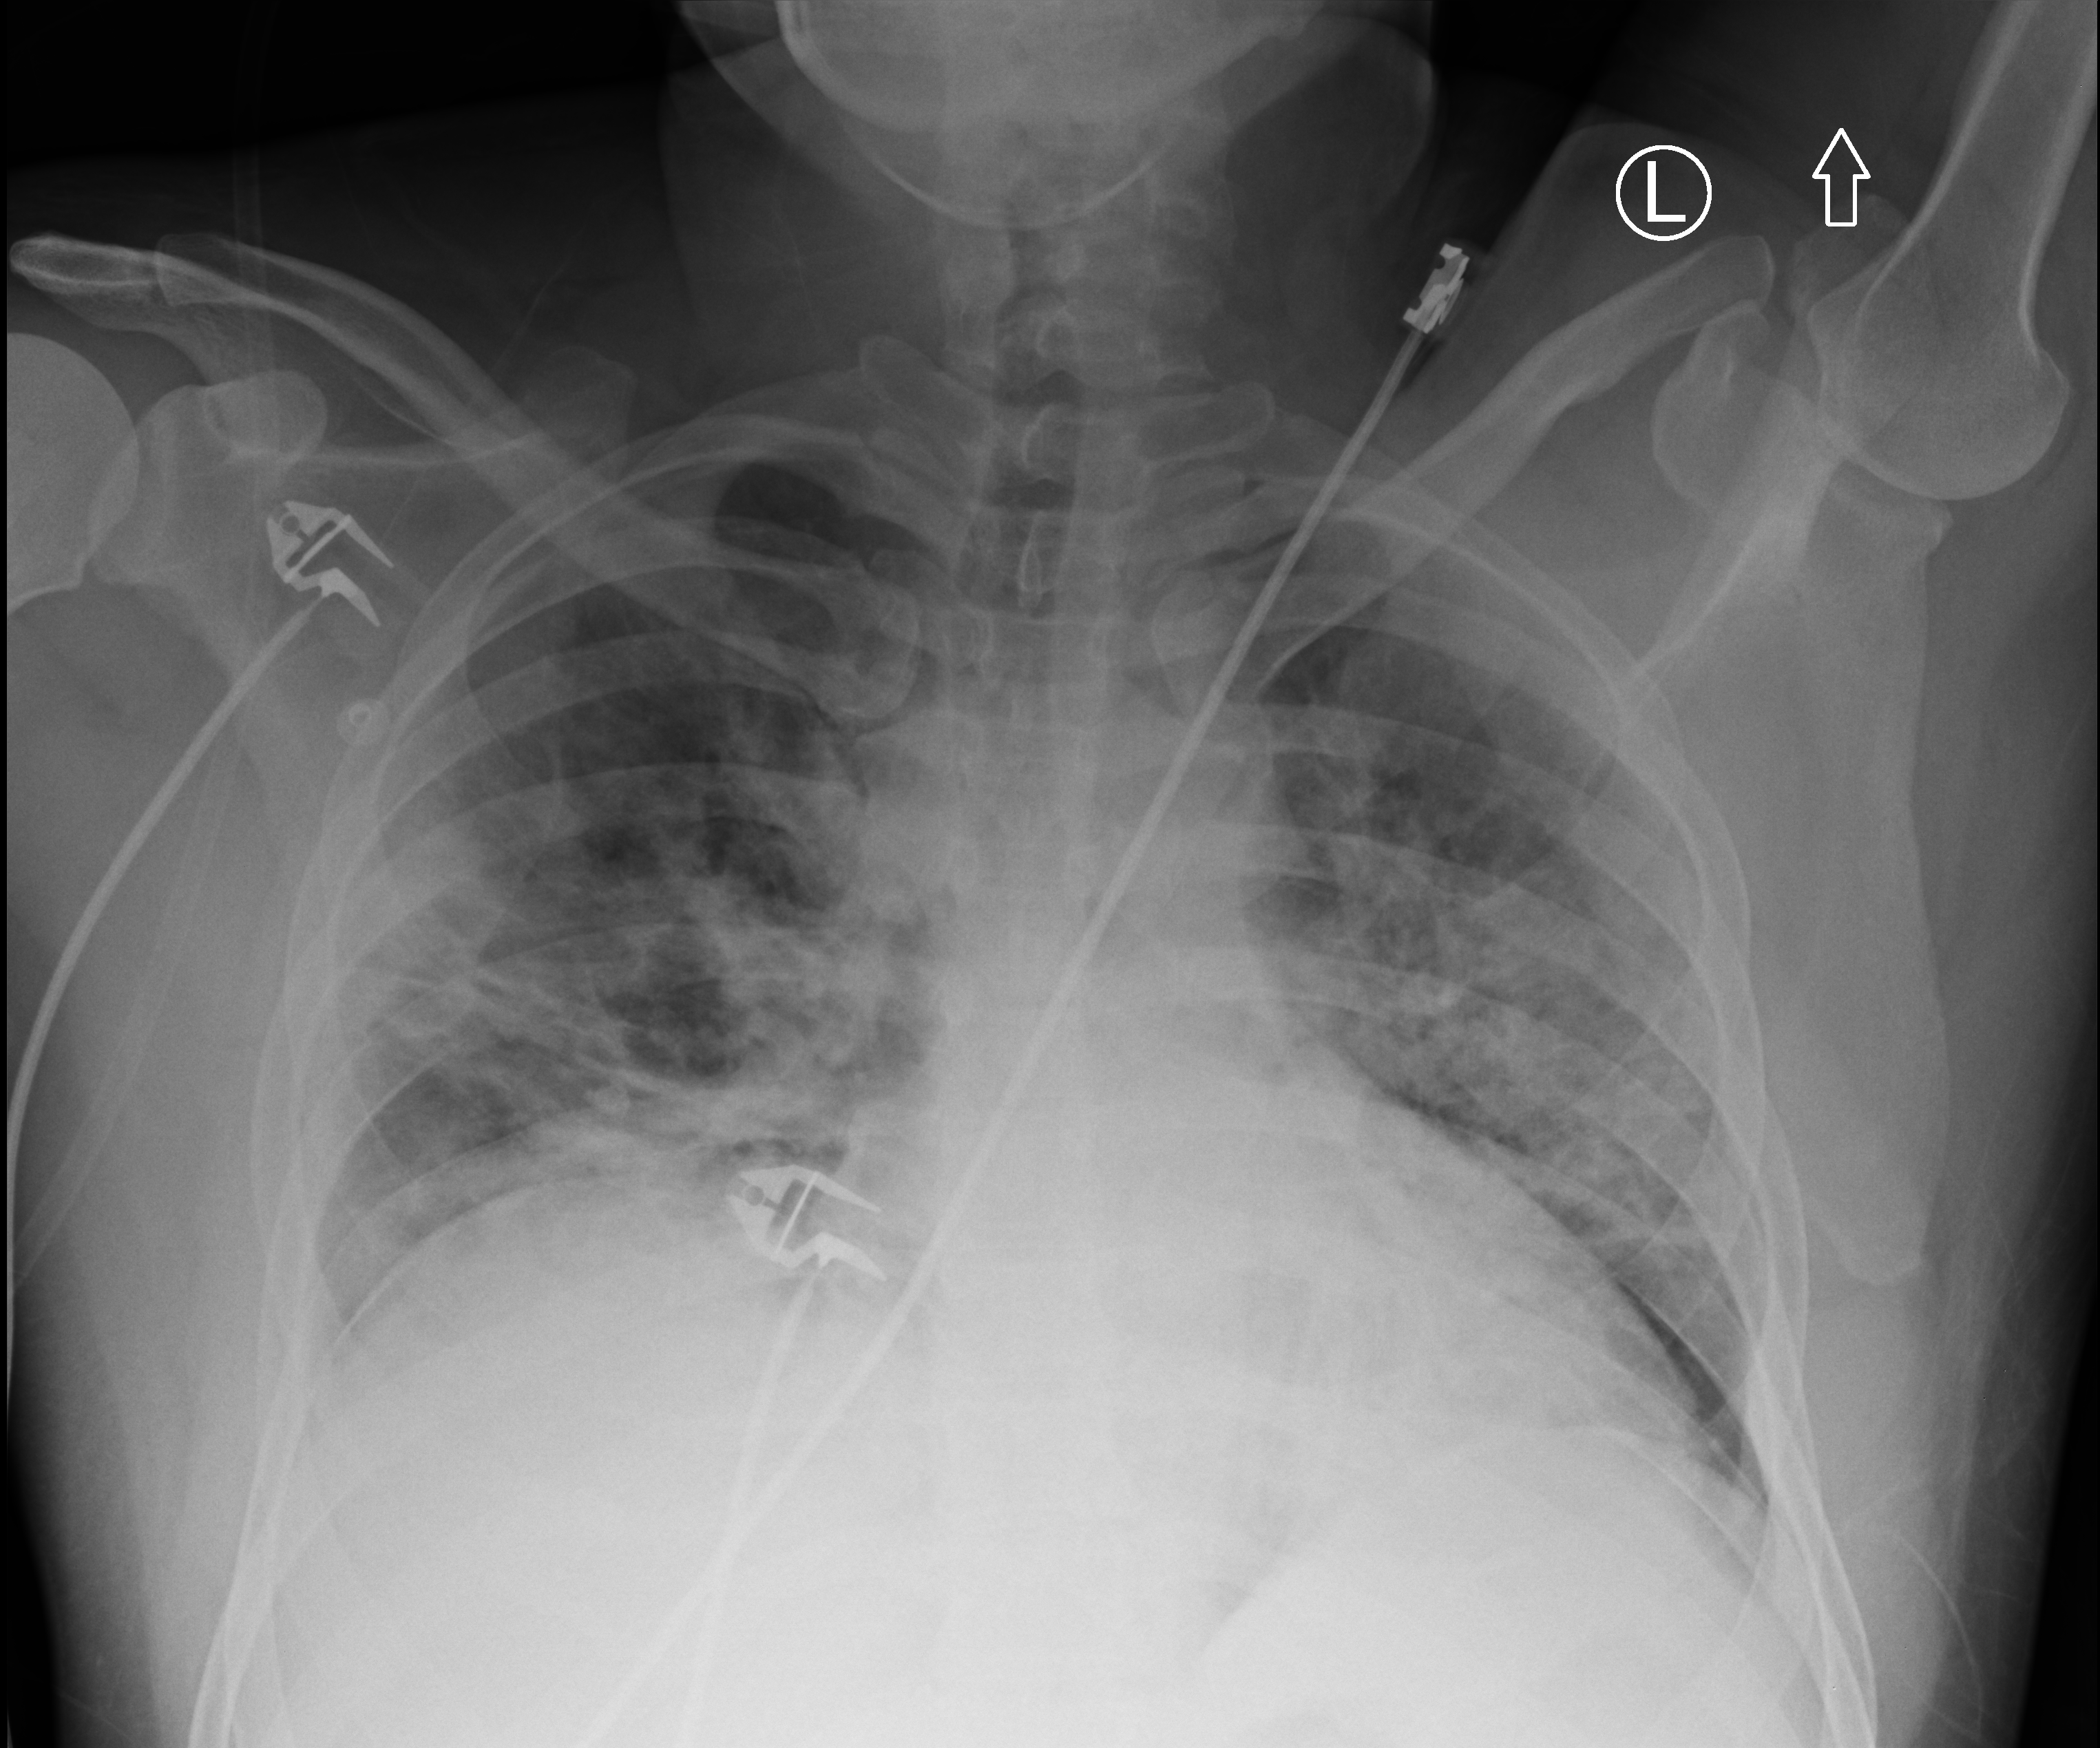
Bedside chest radiograph (computed radiography); anteroposterior (AP) projection. Patient hospitalised with COVID-19; male, aged 18–59 years.
From the hospital-stay record, not from the radiograph (when in the stay this image was taken is not recorded):
- length of hospital stay: 15 days